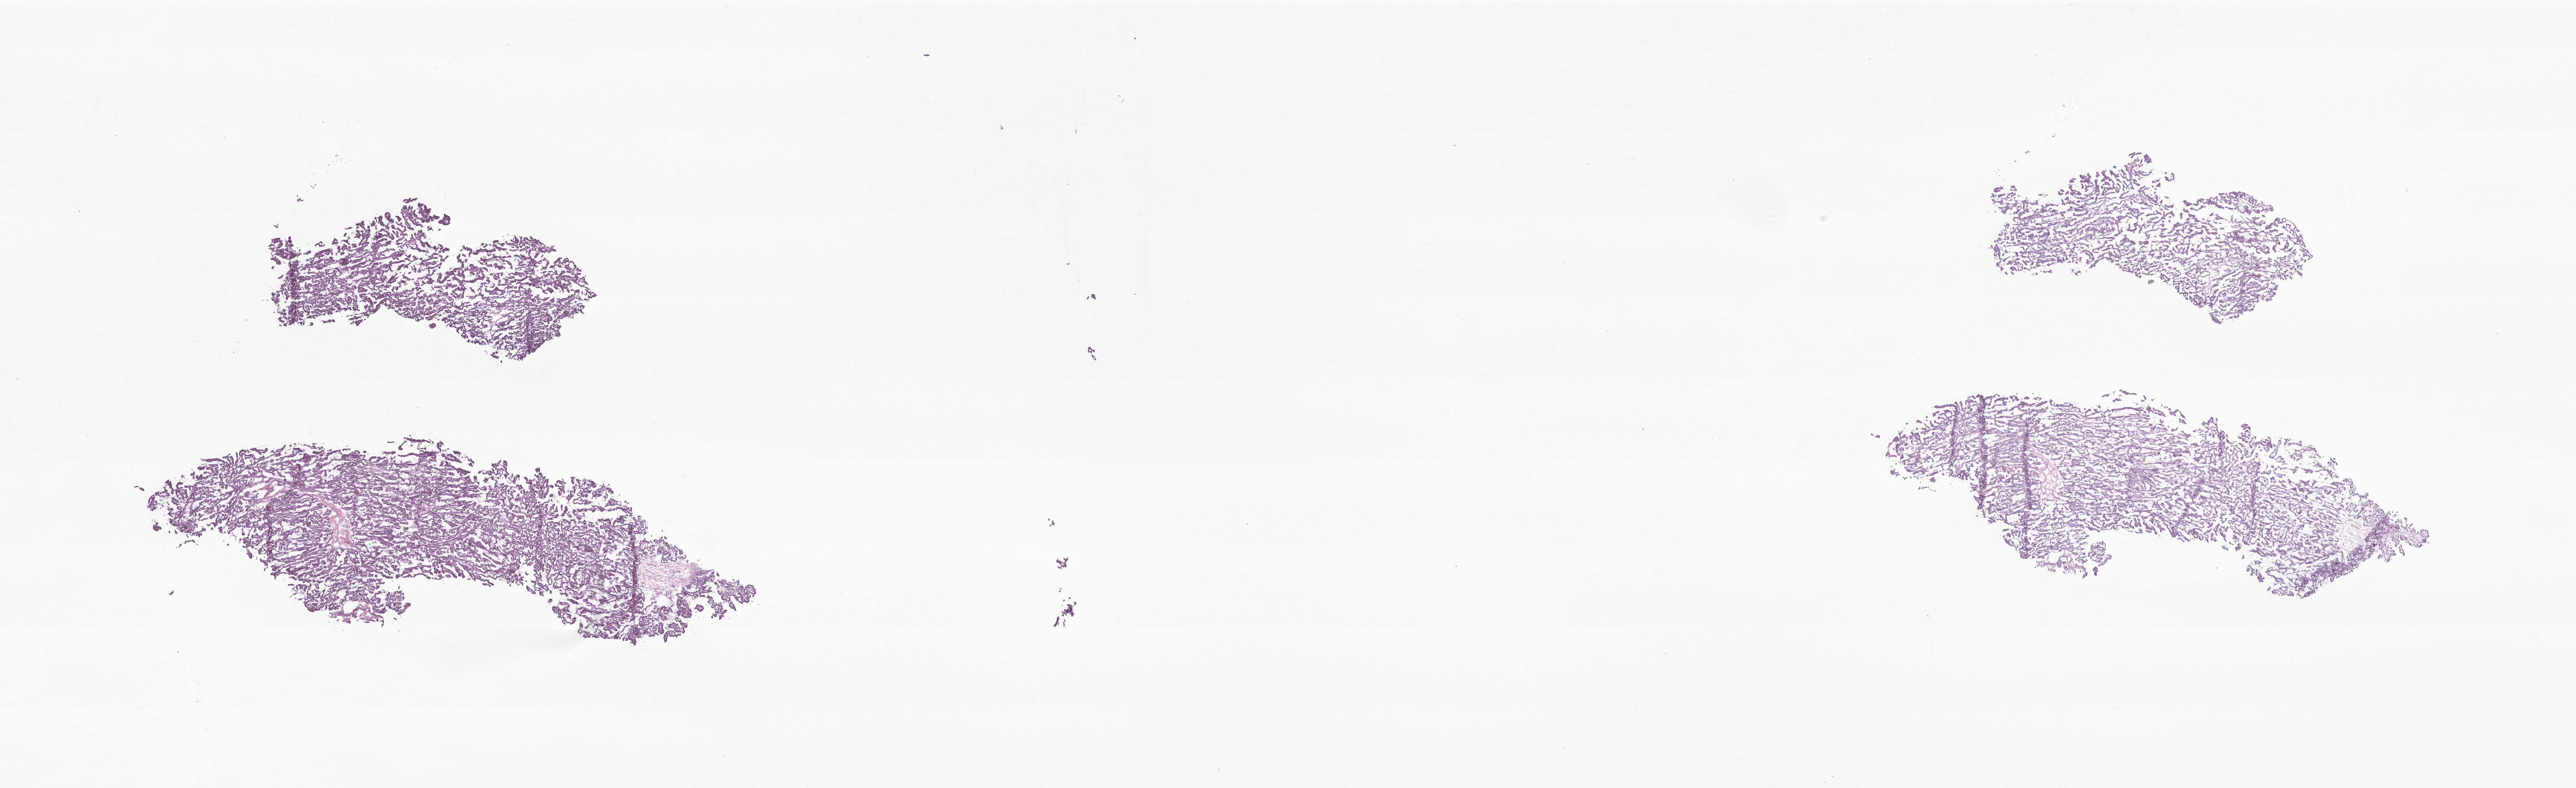
Whole-slide image, H&E stain of tumor tissue from the brain — a low-resolution overview of the entire scanned area, about 33.3 x 10.2 mm; frozen section. Patient: female, age 39 months (3 years 3 months).
Diagnosis: Choroid plexus papilloma, NOS.